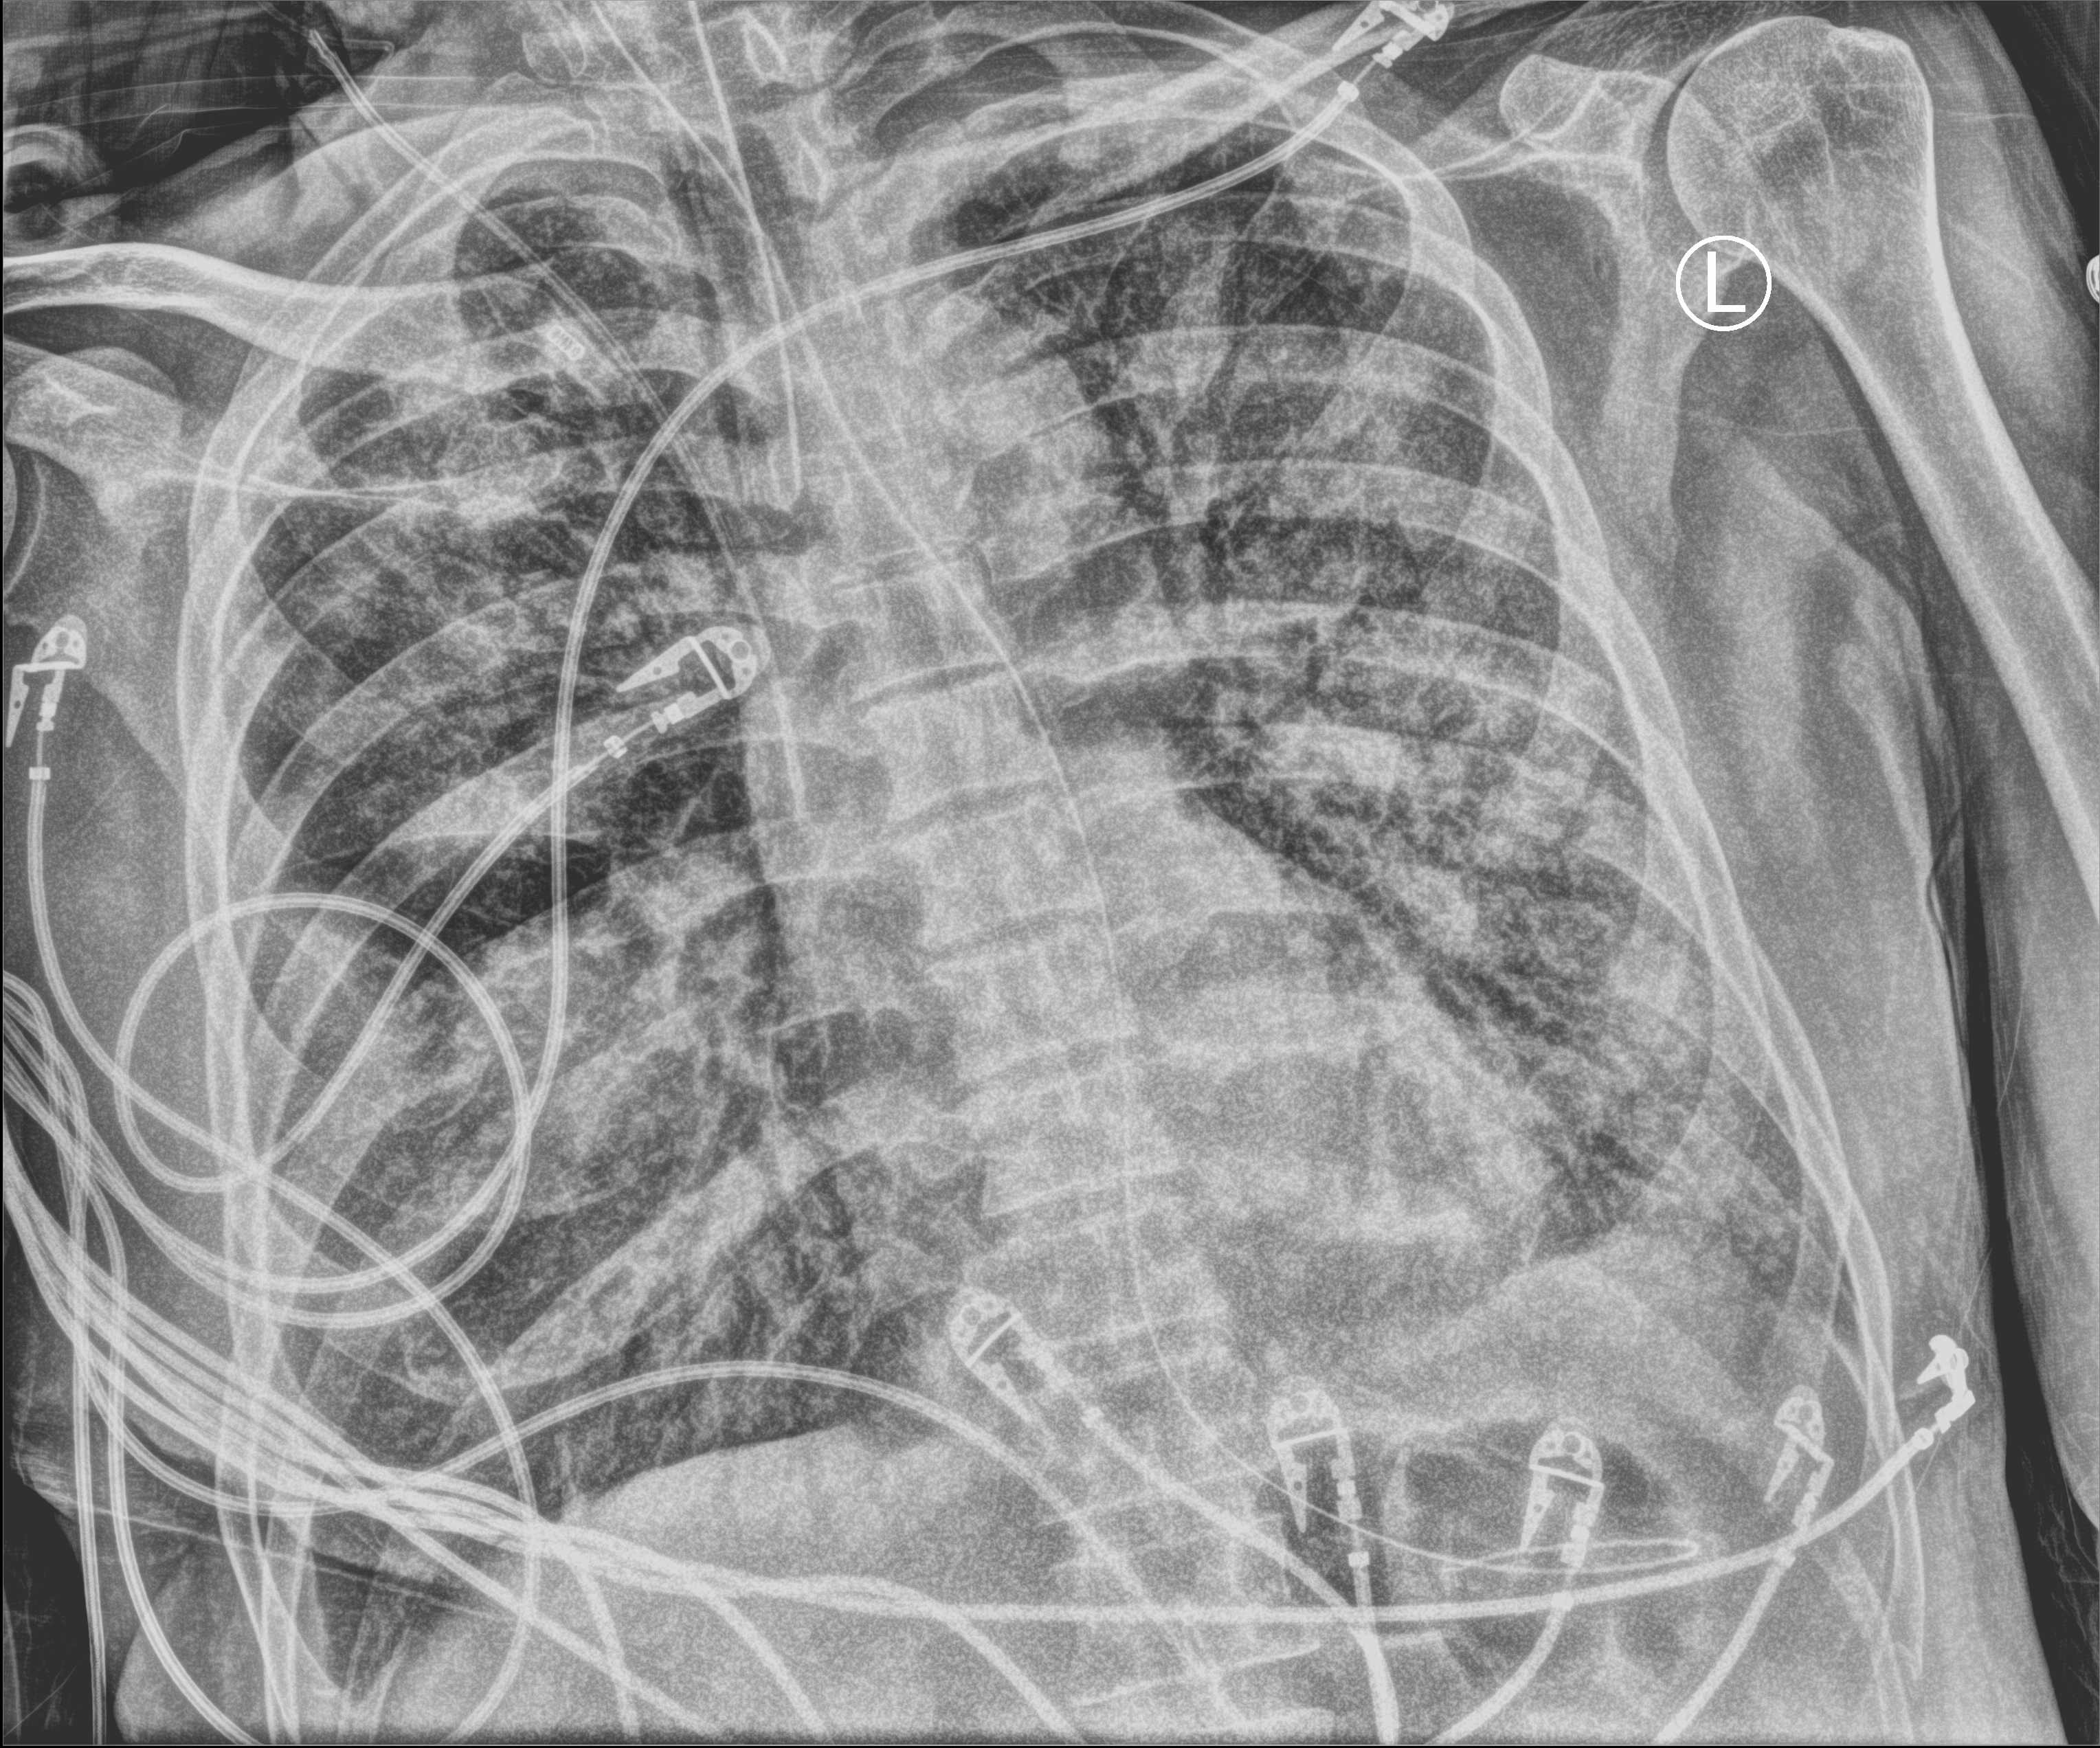
Bedside chest radiograph (computed radiography), anteroposterior (AP) projection. Male patient hospitalised with COVID-19, age 60–74 years.
Hospital-stay facts (about this admission, not read from this image; timing relative to this image not recorded): mechanically ventilated during this hospital stay: yes.